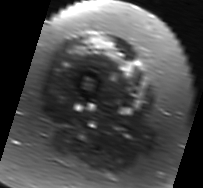
MRI of an extremity soft-tissue mass, one axial slice; position 16 of 91 along the scan axis; T2-weighted fat-saturated; MR volume resampled by the dataset authors to the PET/CT grid (not the native acquisition matrix); 3.27 mm slice thickness; 203 × 188 image matrix, field of view 198 × 184 mm. Female patient. Case-level facts recorded for this patient, not image findings: histological type: malignant solitary fibrous tumor; grade: intermediate; site of the primary tumour: right thigh.
Annotated regions visible in this slice (expert contour drawn on MRI and transferred to this co-registered scan by the dataset authors):
- gross tumour volume including surrounding oedema: box from (x=79, y=35) to (x=134, y=73) px